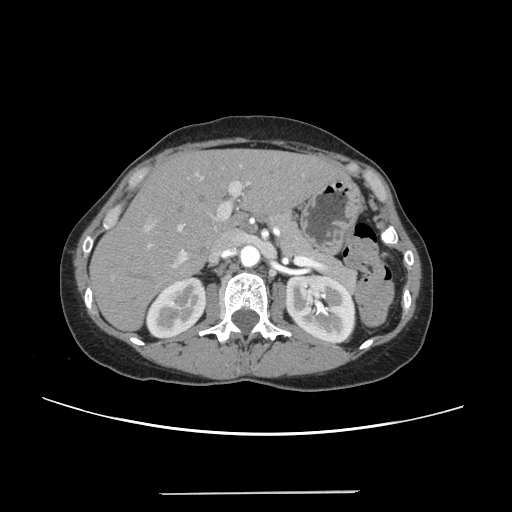
Contrast-enhanced abdominal CT, one axial slice. 120 kVp. Soft-tissue window (W 400 / L 40 HU). 1.25 mm slice thickness. 512 × 512 image matrix, field of view 371 × 371 mm. Female patient, age 60 years. Case-level facts recorded for this patient, not image findings: diagnosis: colorectal cancer liver metastases, imaged before liver resection; multiple liver metastases: no; largest metastasis: 1.5 cm; chemotherapy before resection: yes.
Outlined on this slice (outlined manually by an expert reader):
- liver: box from (x=92, y=150) to (x=344, y=329) px
- planned liver remnant (the part of the liver to remain after resection): (x=92, y=150)–(x=343, y=329)
- portal vein (with intrahepatic branches): (x=143, y=164)–(x=251, y=266)